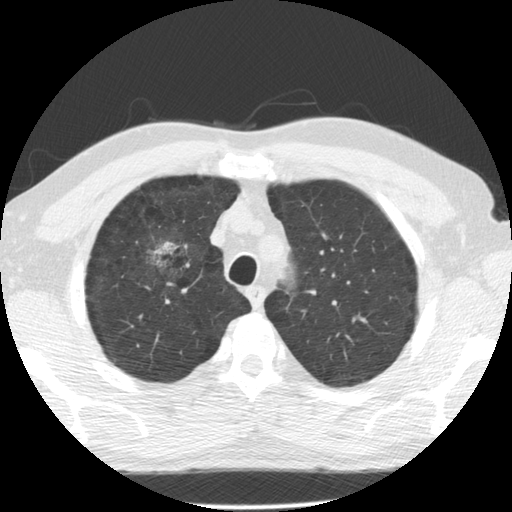
Chest CT (low-dose screening protocol), one axial image. Second annual screen. Lung window (W 1500 / L -600 HU). 2.5 mm slice thickness. Standard (soft-tissue) reconstruction kernel (STANDARD). 512 × 512 image matrix. Male participant, aged 60 years at enrolment.
Expert reader's lesion annotation, bounding box (x1, y1, x2, y2) in pixels: (134, 228, 191, 287). The exam's reader record, not a measurement of the box and not confirmed to be the same lesion: non-calcified nodule or mass ≥4 mm, right upper lobe, poorly defined margins, mixed attenuation, pre-existing on the prior screen: yes; interval growth: yes.